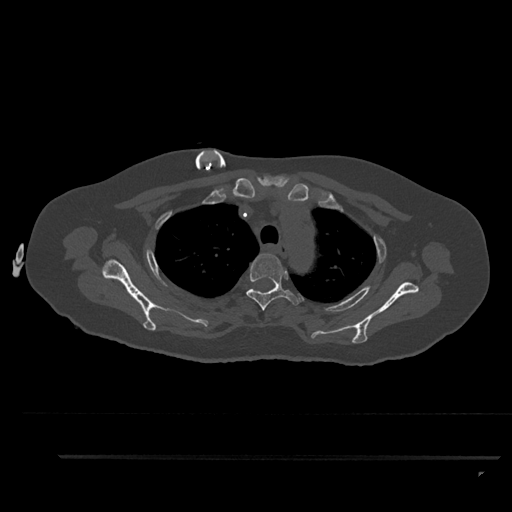
CT including the spine, one axial slice. Position 684 of 797 along the scan axis. Reconstruction kernel Br40s/3. 120 kVp. Bone window (W 1800 / L 400 HU). 0.5 mm slice thickness. 512 × 512 image matrix, field of view 408 × 408 mm. Patient: female, 44 years. Case-level facts recorded for this patient, not image findings: primary cancer: renal; vertebrae with lytic lesions (as recorded): L1.
Annotated regions visible in this slice (semi-automatically segmented with operator editing):
- T3 vertebra: bounding box (x1, y1, x2, y2) in pixels: (246, 254, 299, 311)